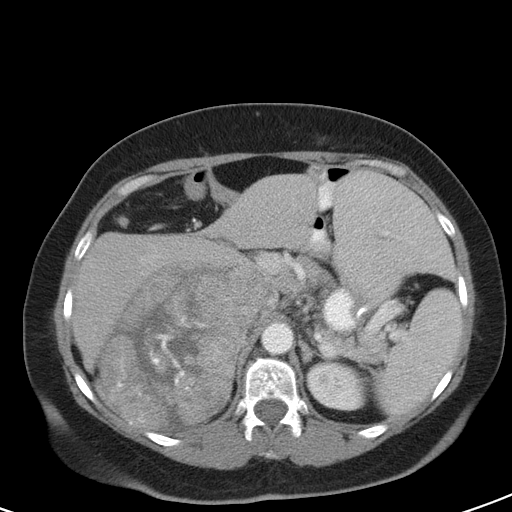
Contrast-enhanced abdominal CT, one axial slice; slice 73 of 126 in the series (ordered by position); 120 kVp; intravenous contrast given; soft-tissue window (W 400 / L 40 HU); 5 mm slice thickness; 512 × 512 image matrix. Female patient, age 51 years. From the clinical record (not read from this slice): diagnosis: adrenocortical carcinoma; tumour side: right adrenal; tumour size at pathology: 17 cm; Ki-67 index: 12 %; stage (as recorded): 2.
Annotated regions visible in this slice (semi-automatic segmentation, software-assisted and operator-edited):
- mass: bounding box (x1, y1, x2, y2) in pixels: (100, 265, 264, 424)